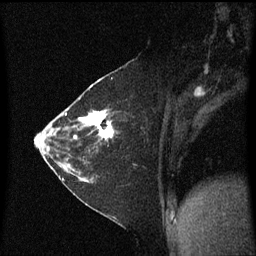
Breast MRI (dynamic contrast-enhanced), one sagittal slice. Position 31 of 60 along the scan axis. Dynamic contrast-enhanced series, image 2 of 3 at this slice position (ordered by acquisition). 1.5 T. TE 4.2 ms, TR 8.4 ms. 2 mm slice thickness. 256 × 256 image matrix, field of view 200 × 200 mm. Patient: female, 36 years. From the clinical record (not read from this slice): setting: breast cancer imaged before/during neoadjuvant chemotherapy; receptor status: HR-positive, HER2-negative.
Annotated regions visible in this slice (semi-automatically segmented with operator editing):
- analysis volume of interest (the breast-tissue region the enhancement analysis was run in; not a lesion): bounding box (x1, y1, x2, y2) in pixels: (66, 102, 115, 179)
- tumour enhancement mask (voxels above the 70 % enhancement threshold inside the analysis volume of interest): (66, 110, 115, 141)